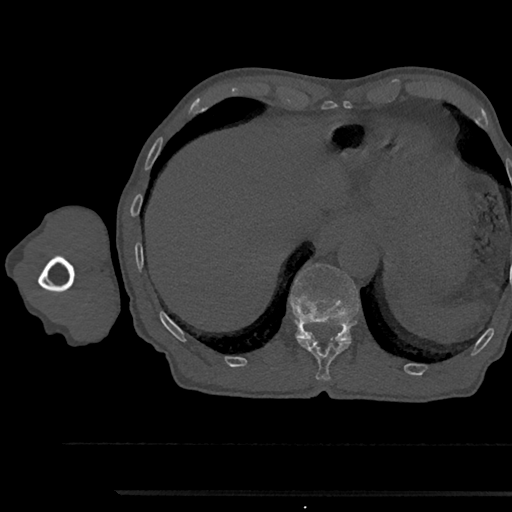
CT including the spine, one axial slice; slice 752 of 797 in the series (ordered by position); 120 kVp; bone window (W 1800 / L 400 HU); 0.5 mm slice thickness; 512 × 512 image matrix. Male patient, age 79 years. From the clinical record (not read from this slice): primary cancer: prostate.
Outlined on this slice (semi-automatic segmentation, software-assisted and operator-edited):
- T11 vertebra: bounding box [x1, y1, x2, y2] px = [298, 339, 349, 381]
- T12 vertebra: [289, 264, 359, 342]